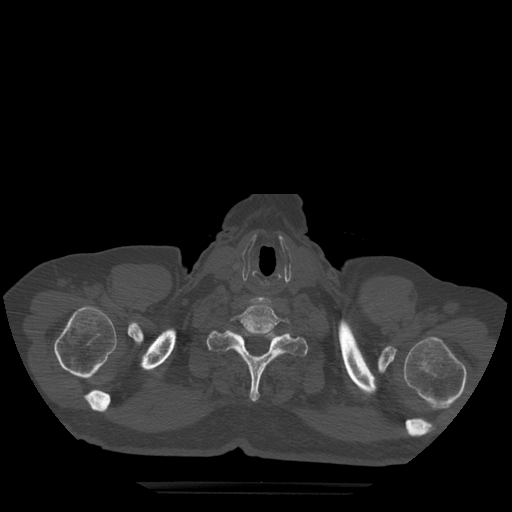
CT including the spine, one axial slice. Position 445 of 522 along the scan axis. Bone window (W 1800 / L 400 HU). 512 × 512 image matrix. Patient age 72 years. Case-level facts recorded for this patient, not image findings: primary cancer: prostate.
Structures marked on this image (semi-automatically segmented with operator editing):
- T1 vertebra: box from (x=207, y=330) to (x=308, y=402) px